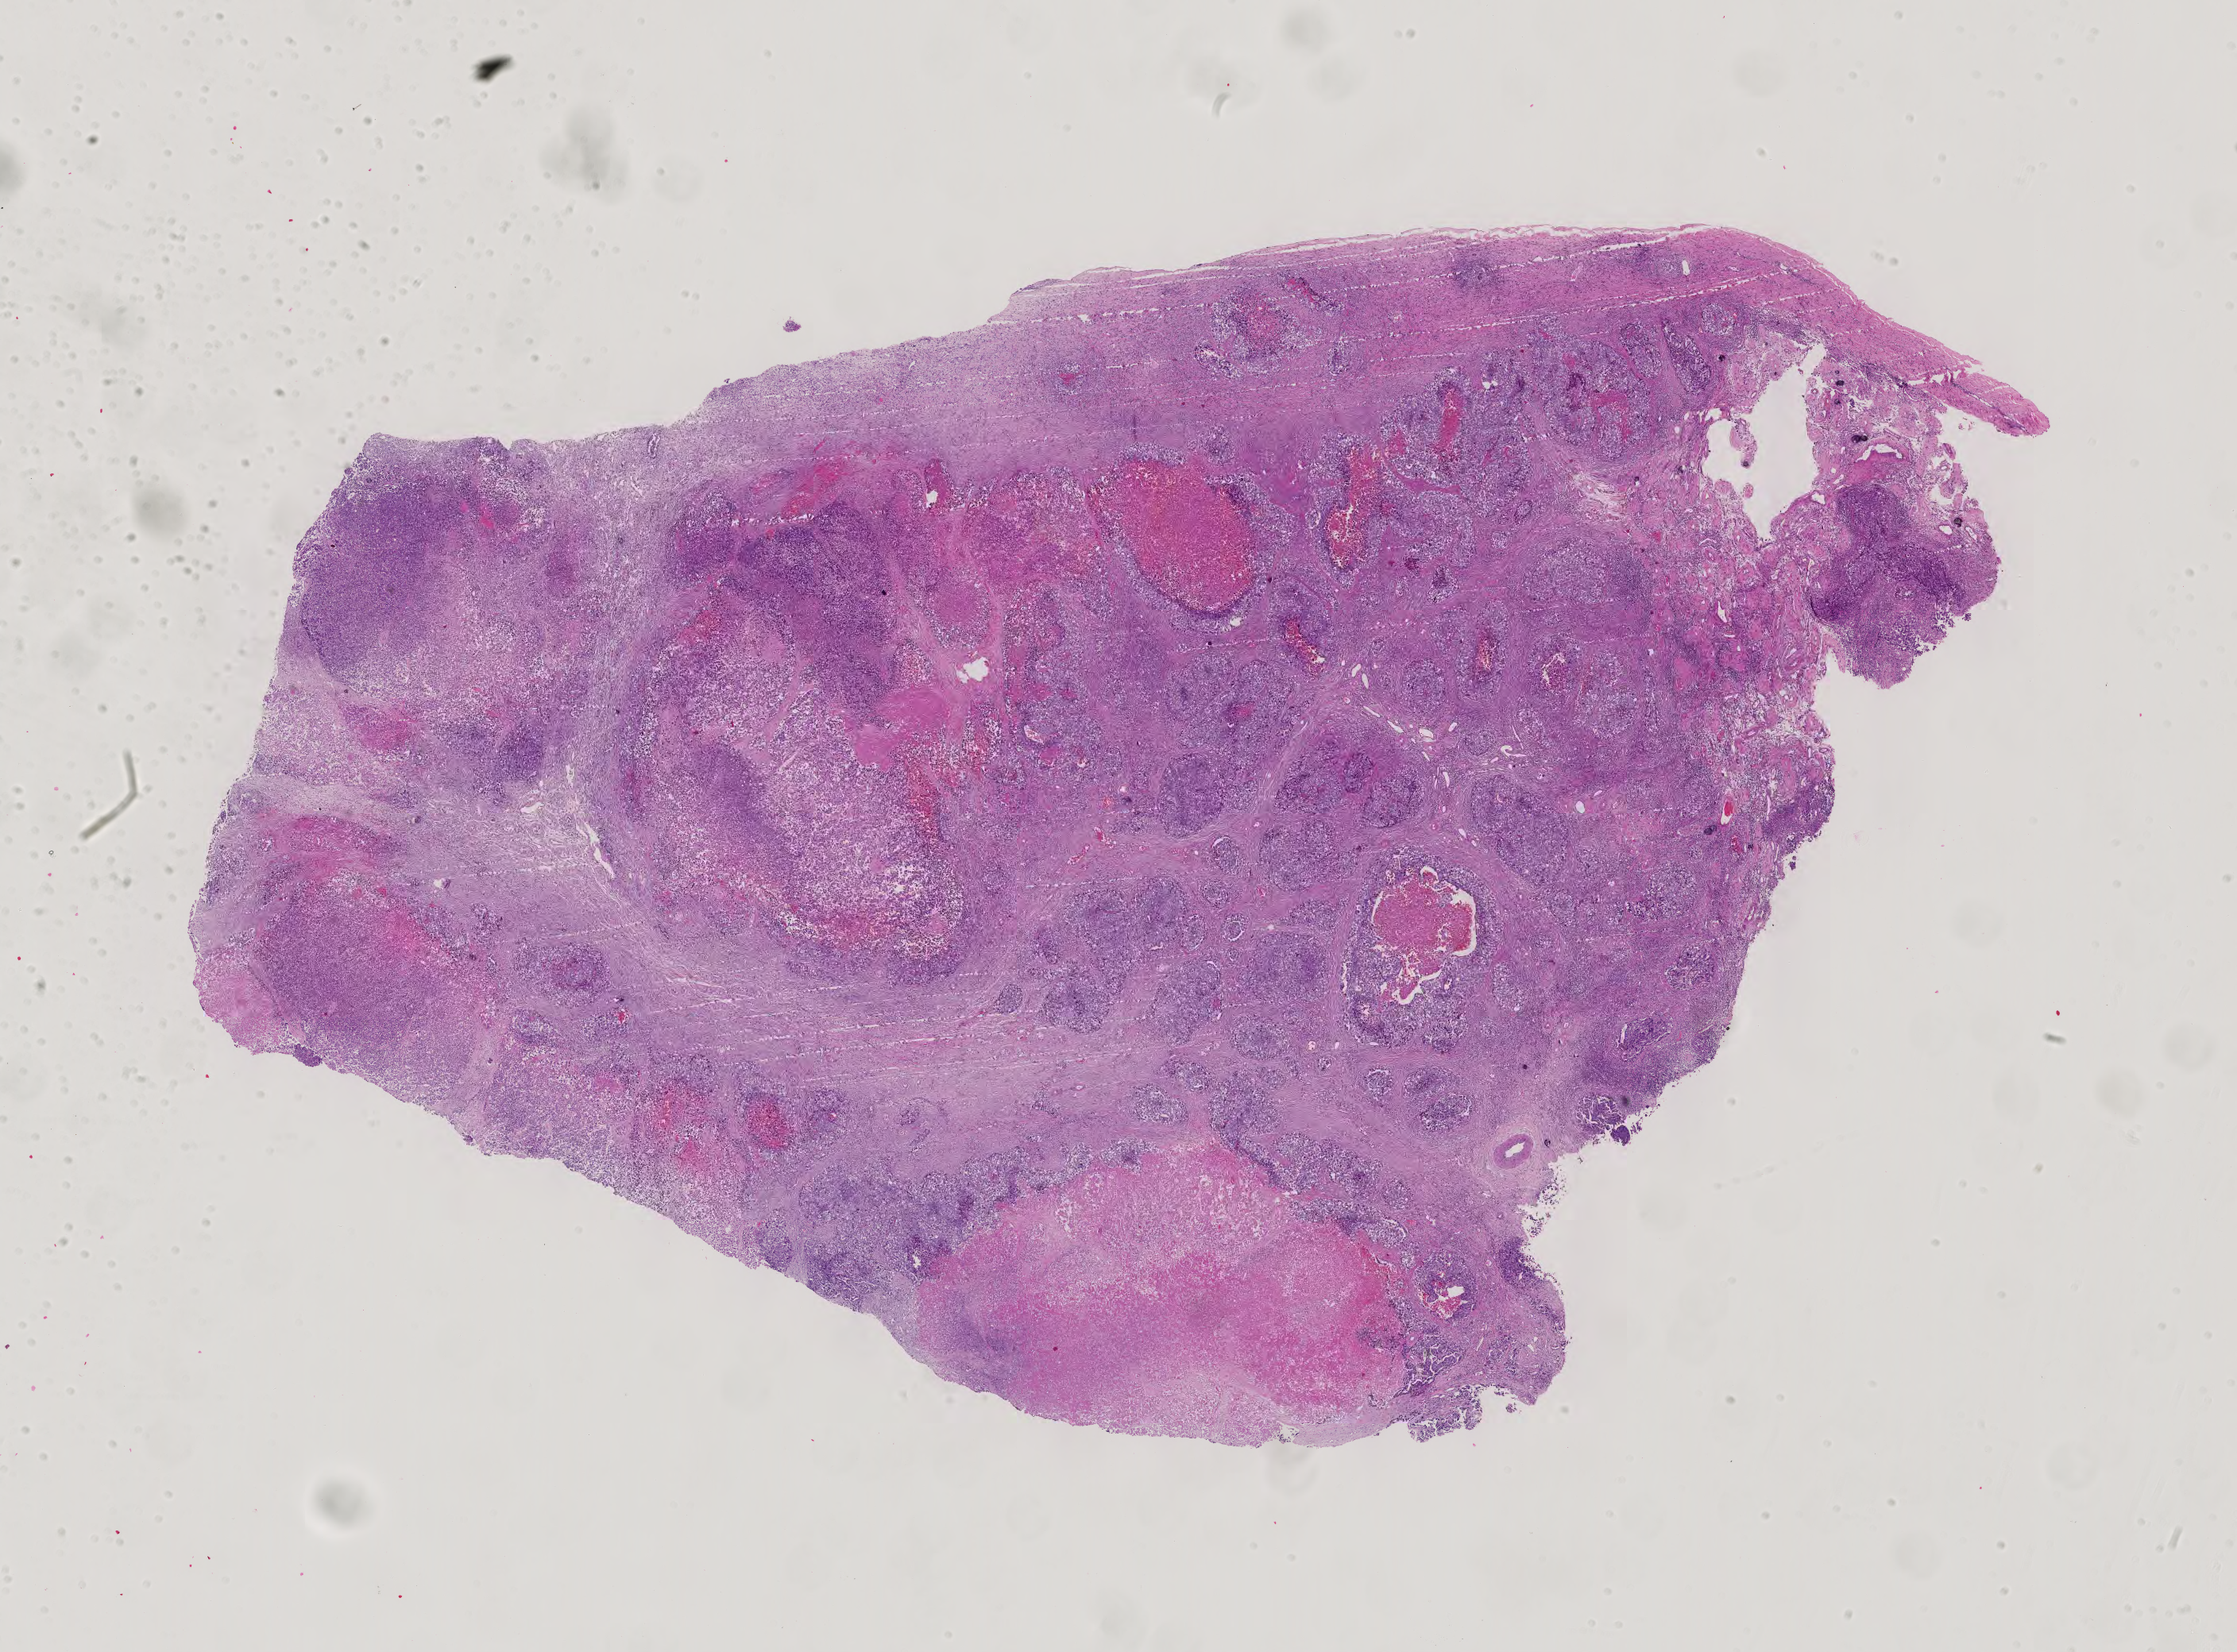
Whole-slide histology image, H&E — low-resolution overview of the scanned area, about 20.5 x 15.2 mm (from a 40x scan), formalin-fixed paraffin-embedded (FFPE) diagnostic section, testis, primary tumour sample. Male patient; age at initial diagnosis 30 years.
Laterality: right. AJCC pathologic stage: IS (5th edition). Pathologic diagnosis: Seminoma, NOS.